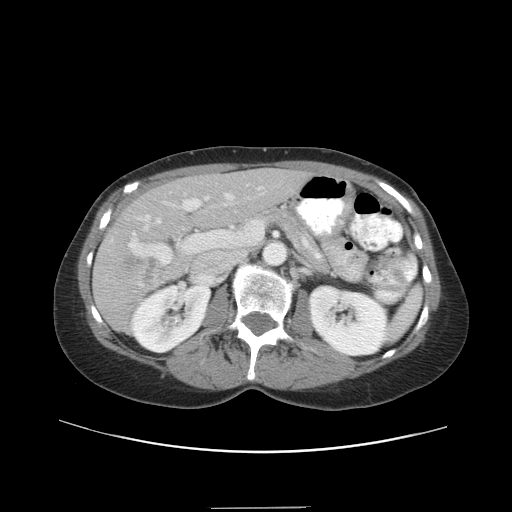
Contrast-enhanced abdominal CT, one axial slice. Position 19 of 38 along the scan axis. Reconstruction kernel STANDARD. 120 kVp. Intravenous contrast given. Soft-tissue window (W 400 / L 40 HU). 5 mm slice thickness. 512 × 512 image matrix, field of view 388 × 388 mm. Female patient, age 64 years. From the clinical record (not read from this slice): diagnosis: colorectal cancer liver metastases, imaged before liver resection; multiple liver metastases: no; largest metastasis: 3.8 cm; disease in both lobes: yes.
Structures marked on this image (manually delineated by an expert):
- hepatic veins: bounding box (x1, y1, x2, y2) in pixels: (140, 186, 263, 286)
- liver: (96, 169, 306, 331)
- planned liver remnant (the part of the liver to remain after resection): (140, 169, 306, 232)
- portal vein (with intrahepatic branches): (128, 190, 267, 264)
- liver metastasis: (123, 256, 159, 283)